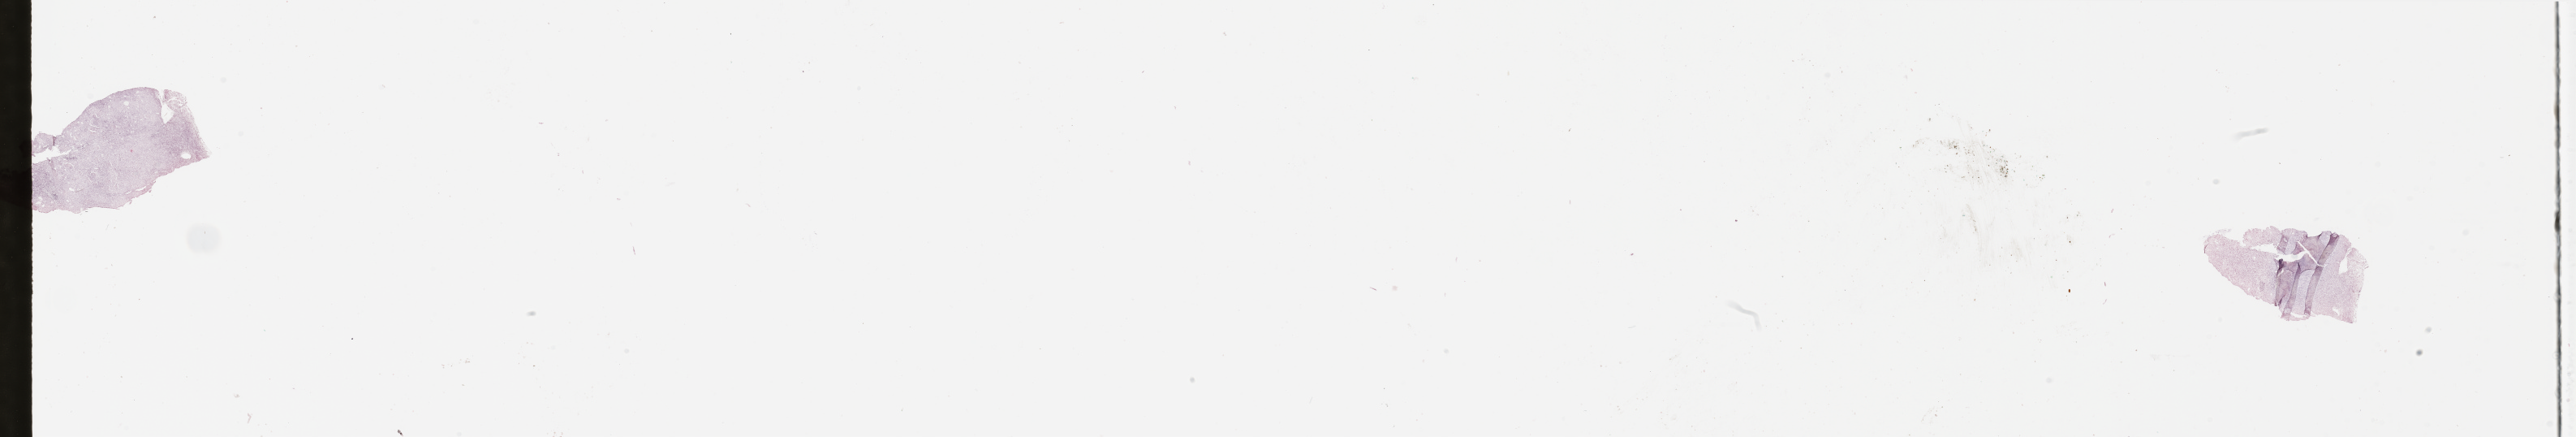
H&E-stained whole-slide image, whole scanned area (about 50.2 x 8.5 mm, from a 20x scan) shown as a low-resolution overview, tumour tissue sample. 60-year-old male patient.
Primary tumour site (as recorded): lower extremity. Patient diagnosis (cohort enrolment): sarcoma (site not recorded at cohort level).